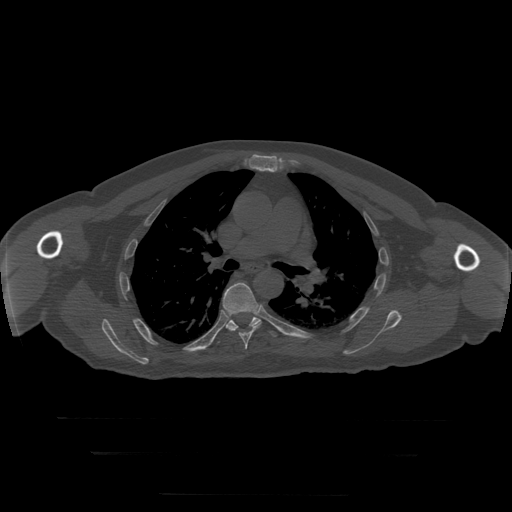
CT including the spine, one axial slice. Position 199 of 397 along the scan axis. Reconstruction kernel STANDARD. Bone window (W 1800 / L 400 HU). 1.25 mm slice thickness. 512 × 512 image matrix, field of view 510 × 510 mm. Patient age 73 years. Case-level facts recorded for this patient, not image findings: primary cancer: prostate.
Structures marked on this image (semi-automatic segmentation, software-assisted and operator-edited):
- T6 vertebra: bounding box [x1, y1, x2, y2] px = [223, 283, 261, 350]
- T7 vertebra: [218, 315, 278, 343]